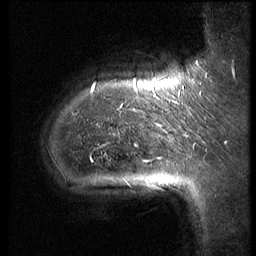
Breast MRI (dynamic contrast-enhanced), one sagittal slice. Position 9 of 62 along the scan axis. 3 images stored at this slice position (order not interpretable as contrast timing). 1.5 T. TE 4.2 ms, TR 9 ms. 2.5 mm slice thickness. 256 × 256 image matrix. Female patient, age 39 years. From the clinical record (not read from this slice): setting: breast cancer imaged before/during neoadjuvant chemotherapy; receptor status: HER2-positive.
Annotated regions visible in this slice (semi-automatically segmented with operator editing):
- analysis volume of interest (the breast-tissue region the enhancement analysis was run in; not a lesion): bounding box [x1, y1, x2, y2] px = [41, 64, 171, 222]
- tumour enhancement mask (voxels above the 140 % enhancement threshold inside the analysis volume of interest): [93, 79, 166, 138]